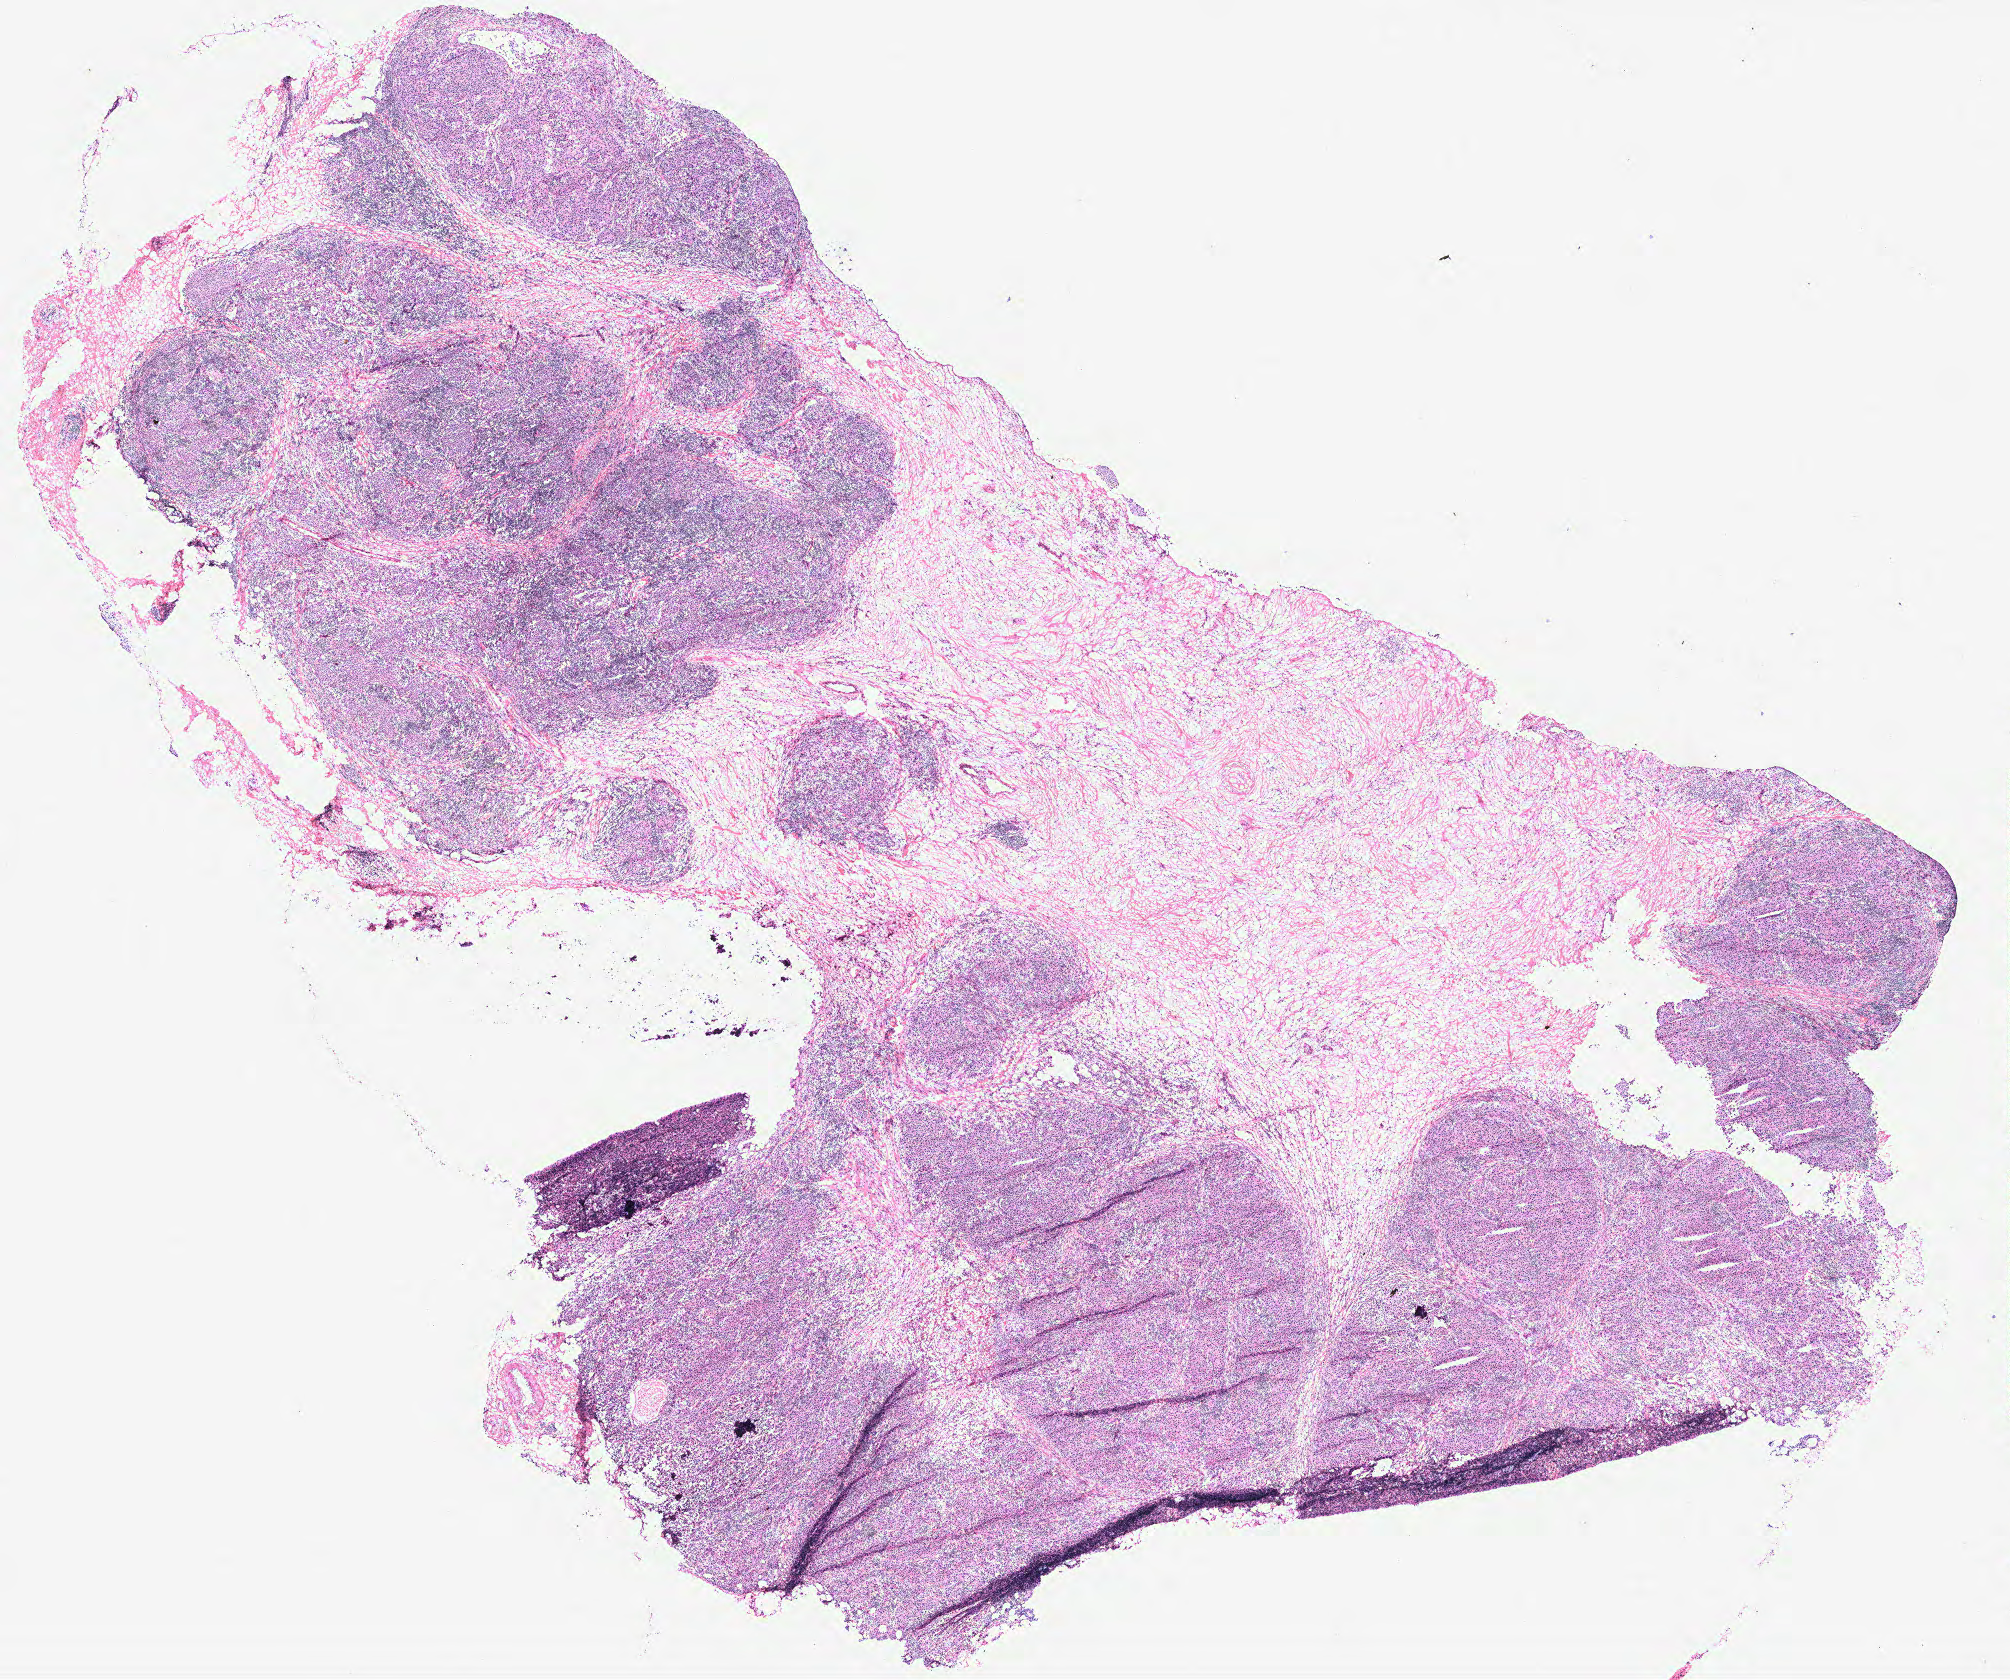
H&E whole-slide image — shown as a low-resolution overview of the whole scanned area (about 16.1 x 13.4 mm). Breast, tissue type not recorded. 64-year-old female patient.
Patient diagnosis: Infiltrating duct carcinoma, NOS.